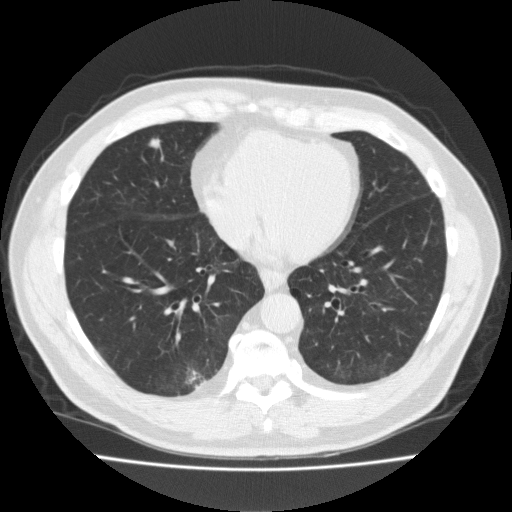
Low-dose screening chest CT, one axial slice. Slice 67 of 184 in the series (ordered by position). Reconstruction kernel FC10. Lung window (W 1500 / L -600 HU). 2 mm slice thickness. 512 × 512 image matrix.
Annotated regions visible in this slice (expert manual segmentation):
- lesion 1 (tumor, middle lobe of right lung): bounding box <150,139,160,148> (left, top, right, bottom; pixels)